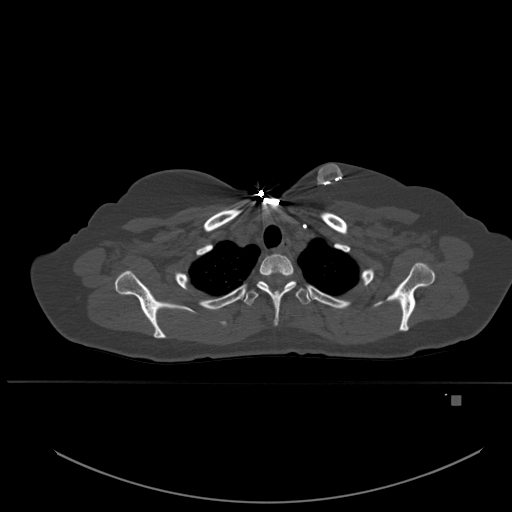
CT including the spine, one axial slice. Position 413 of 651 along the scan axis. Bone window (W 1800 / L 400 HU). 1.5 mm slice thickness. 512 × 512 image matrix. Patient: female, 49 years. From the clinical record (not read from this slice): primary cancer: breast.
Outlined on this slice (semi-automatically segmented with operator editing):
- T1 vertebra: bounding box (x1, y1, x2, y2) in pixels: (257, 254, 296, 325)
- T2 vertebra: (244, 281, 311, 306)